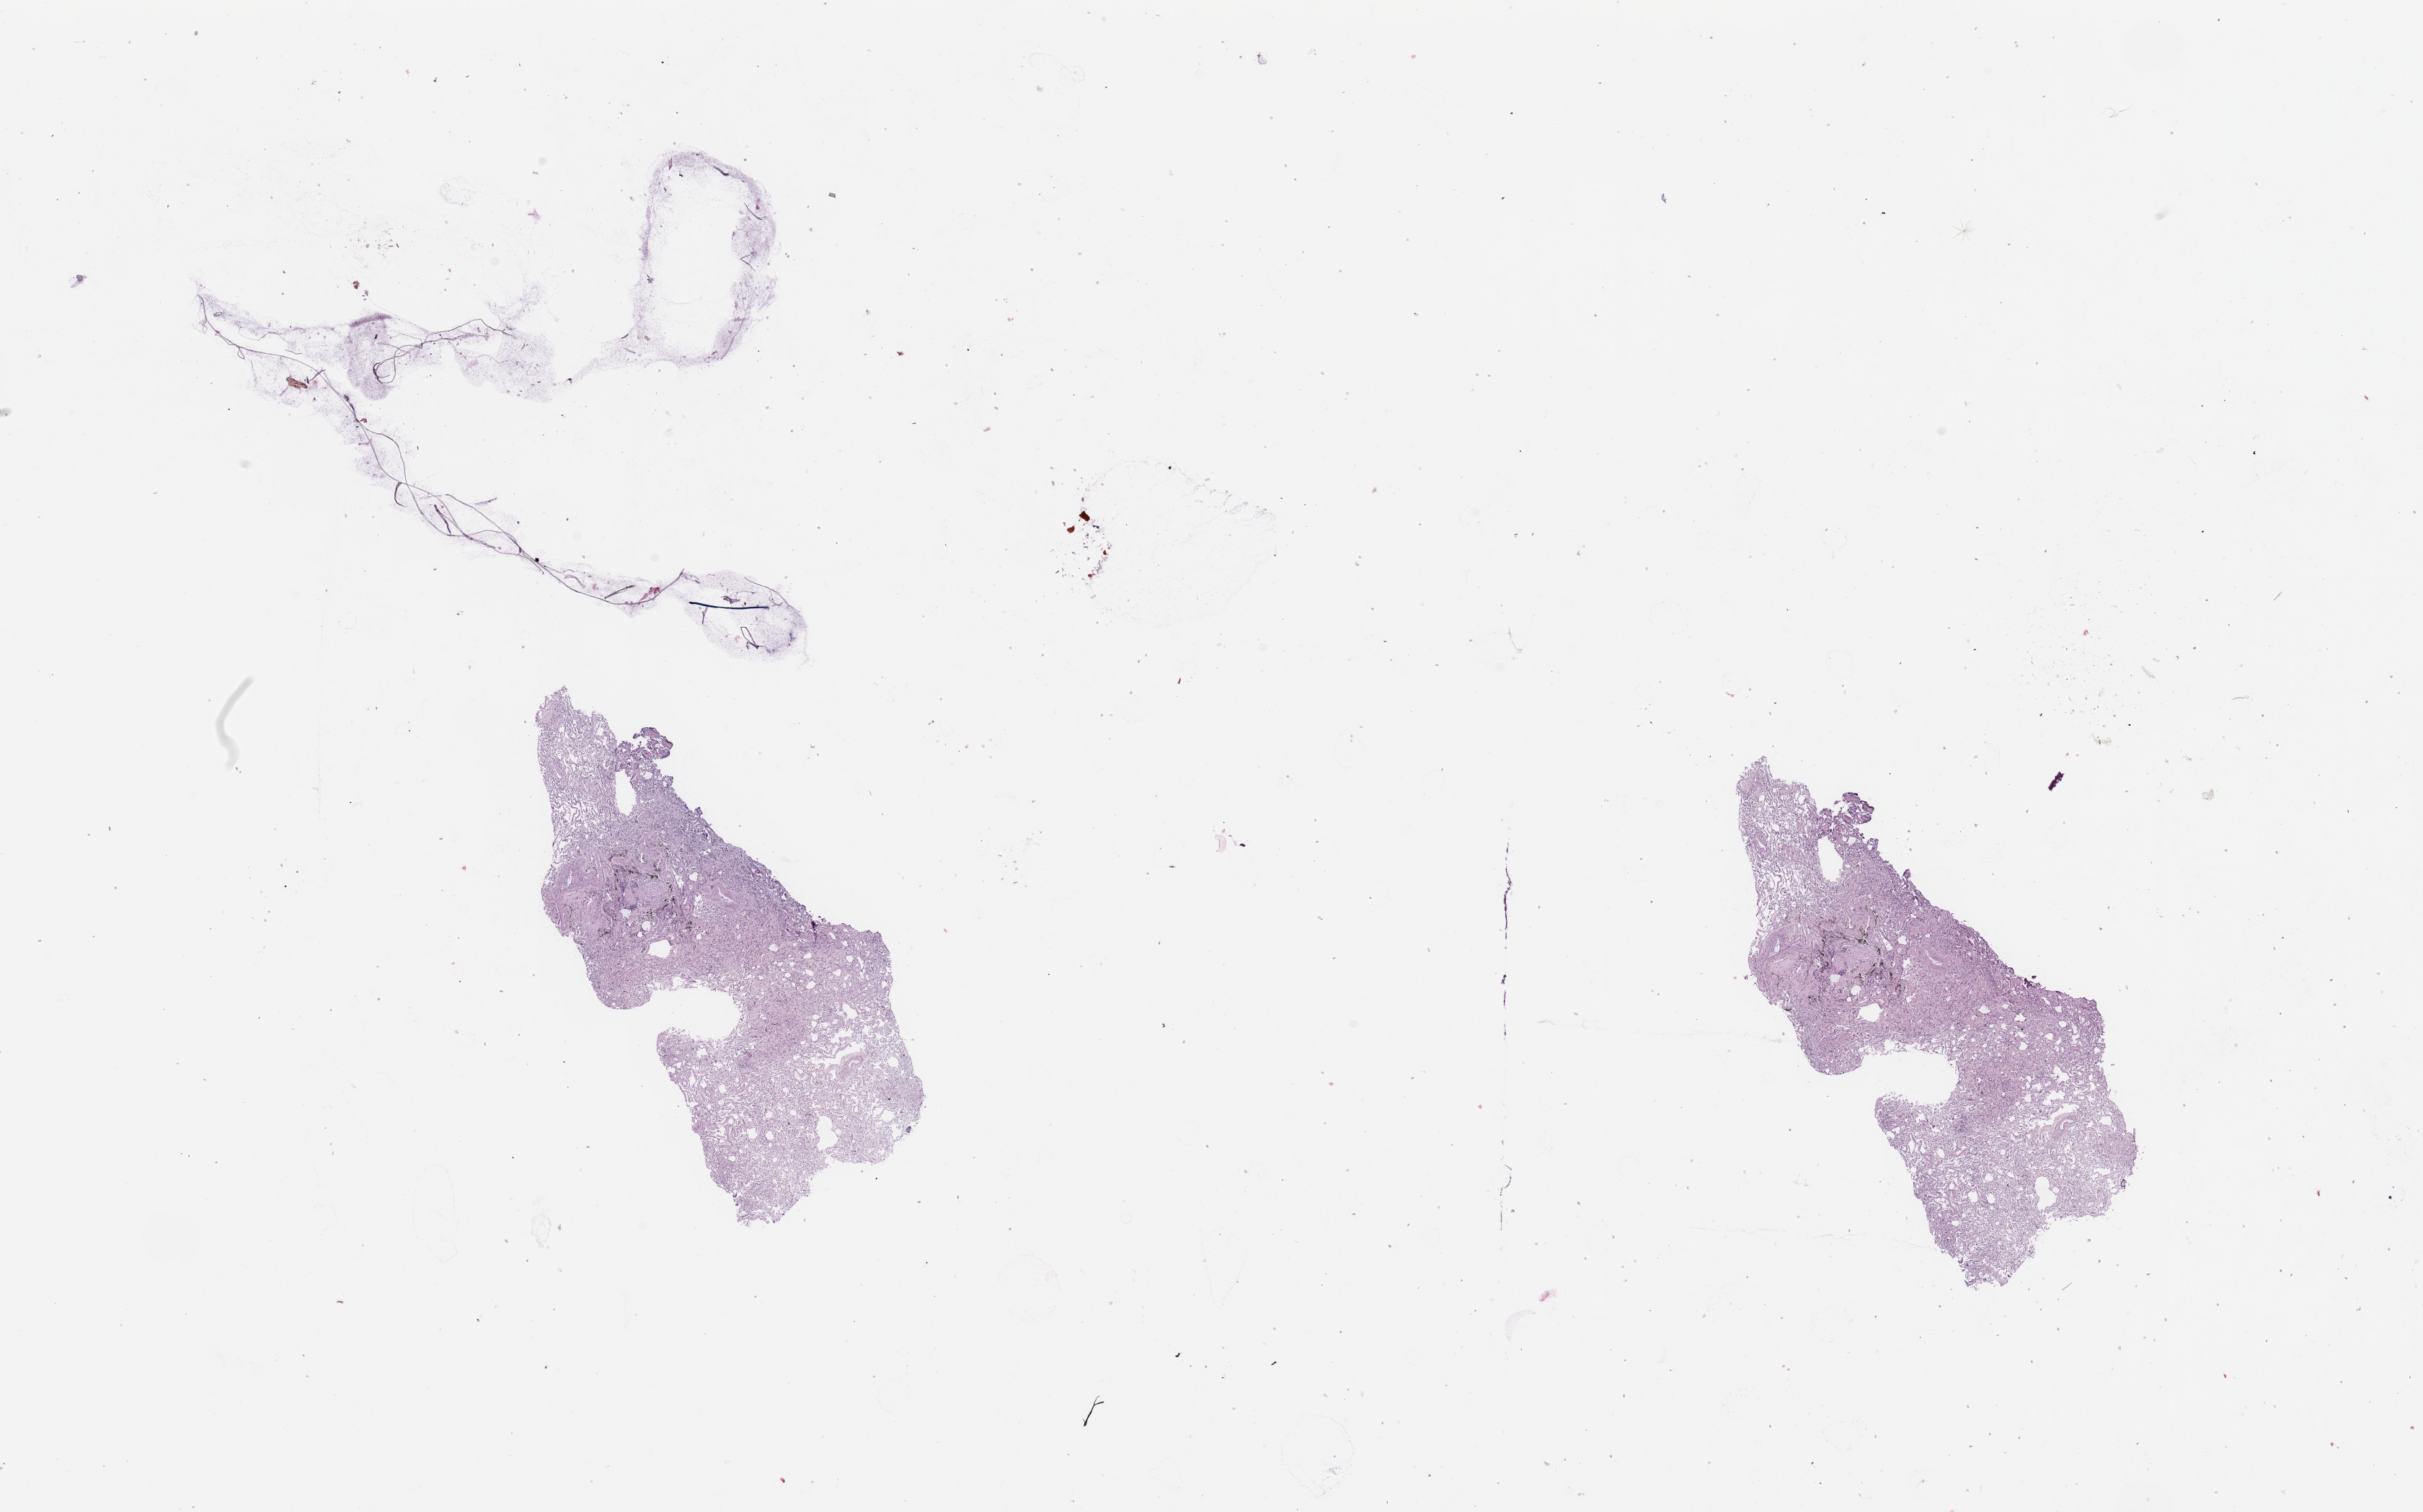
H&E-stained whole-slide image — whole scanned area (about 26.6 x 16.6 mm) shown as a low-resolution overview; normal (non-tumour) tissue sample, lung. Patient: male, age 77 years.
This section: normal (non-tumour) tissue from the same patient. Patient diagnosis: Adenocarcinoma, NOS.